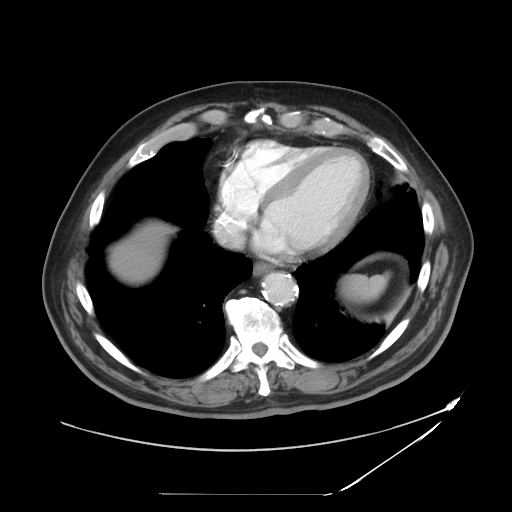
Contrast-enhanced abdominal CT, one axial slice. Slice 43 of 49 in the series (ordered by position). Reconstruction kernel STANDARD. 120 kVp. Intravenous contrast given. Soft-tissue window (W 400 / L 40 HU). 512 × 512 image matrix. Male patient, age 72 years. From the clinical record (not read from this slice): diagnosis: colorectal cancer liver metastases, imaged before liver resection; multiple liver metastases: no.
Annotated regions visible in this slice (manually delineated by an expert):
- liver: bounding box (x1, y1, x2, y2) in pixels: (113, 226, 165, 281)
- planned liver remnant (the part of the liver to remain after resection): (112, 226, 165, 281)